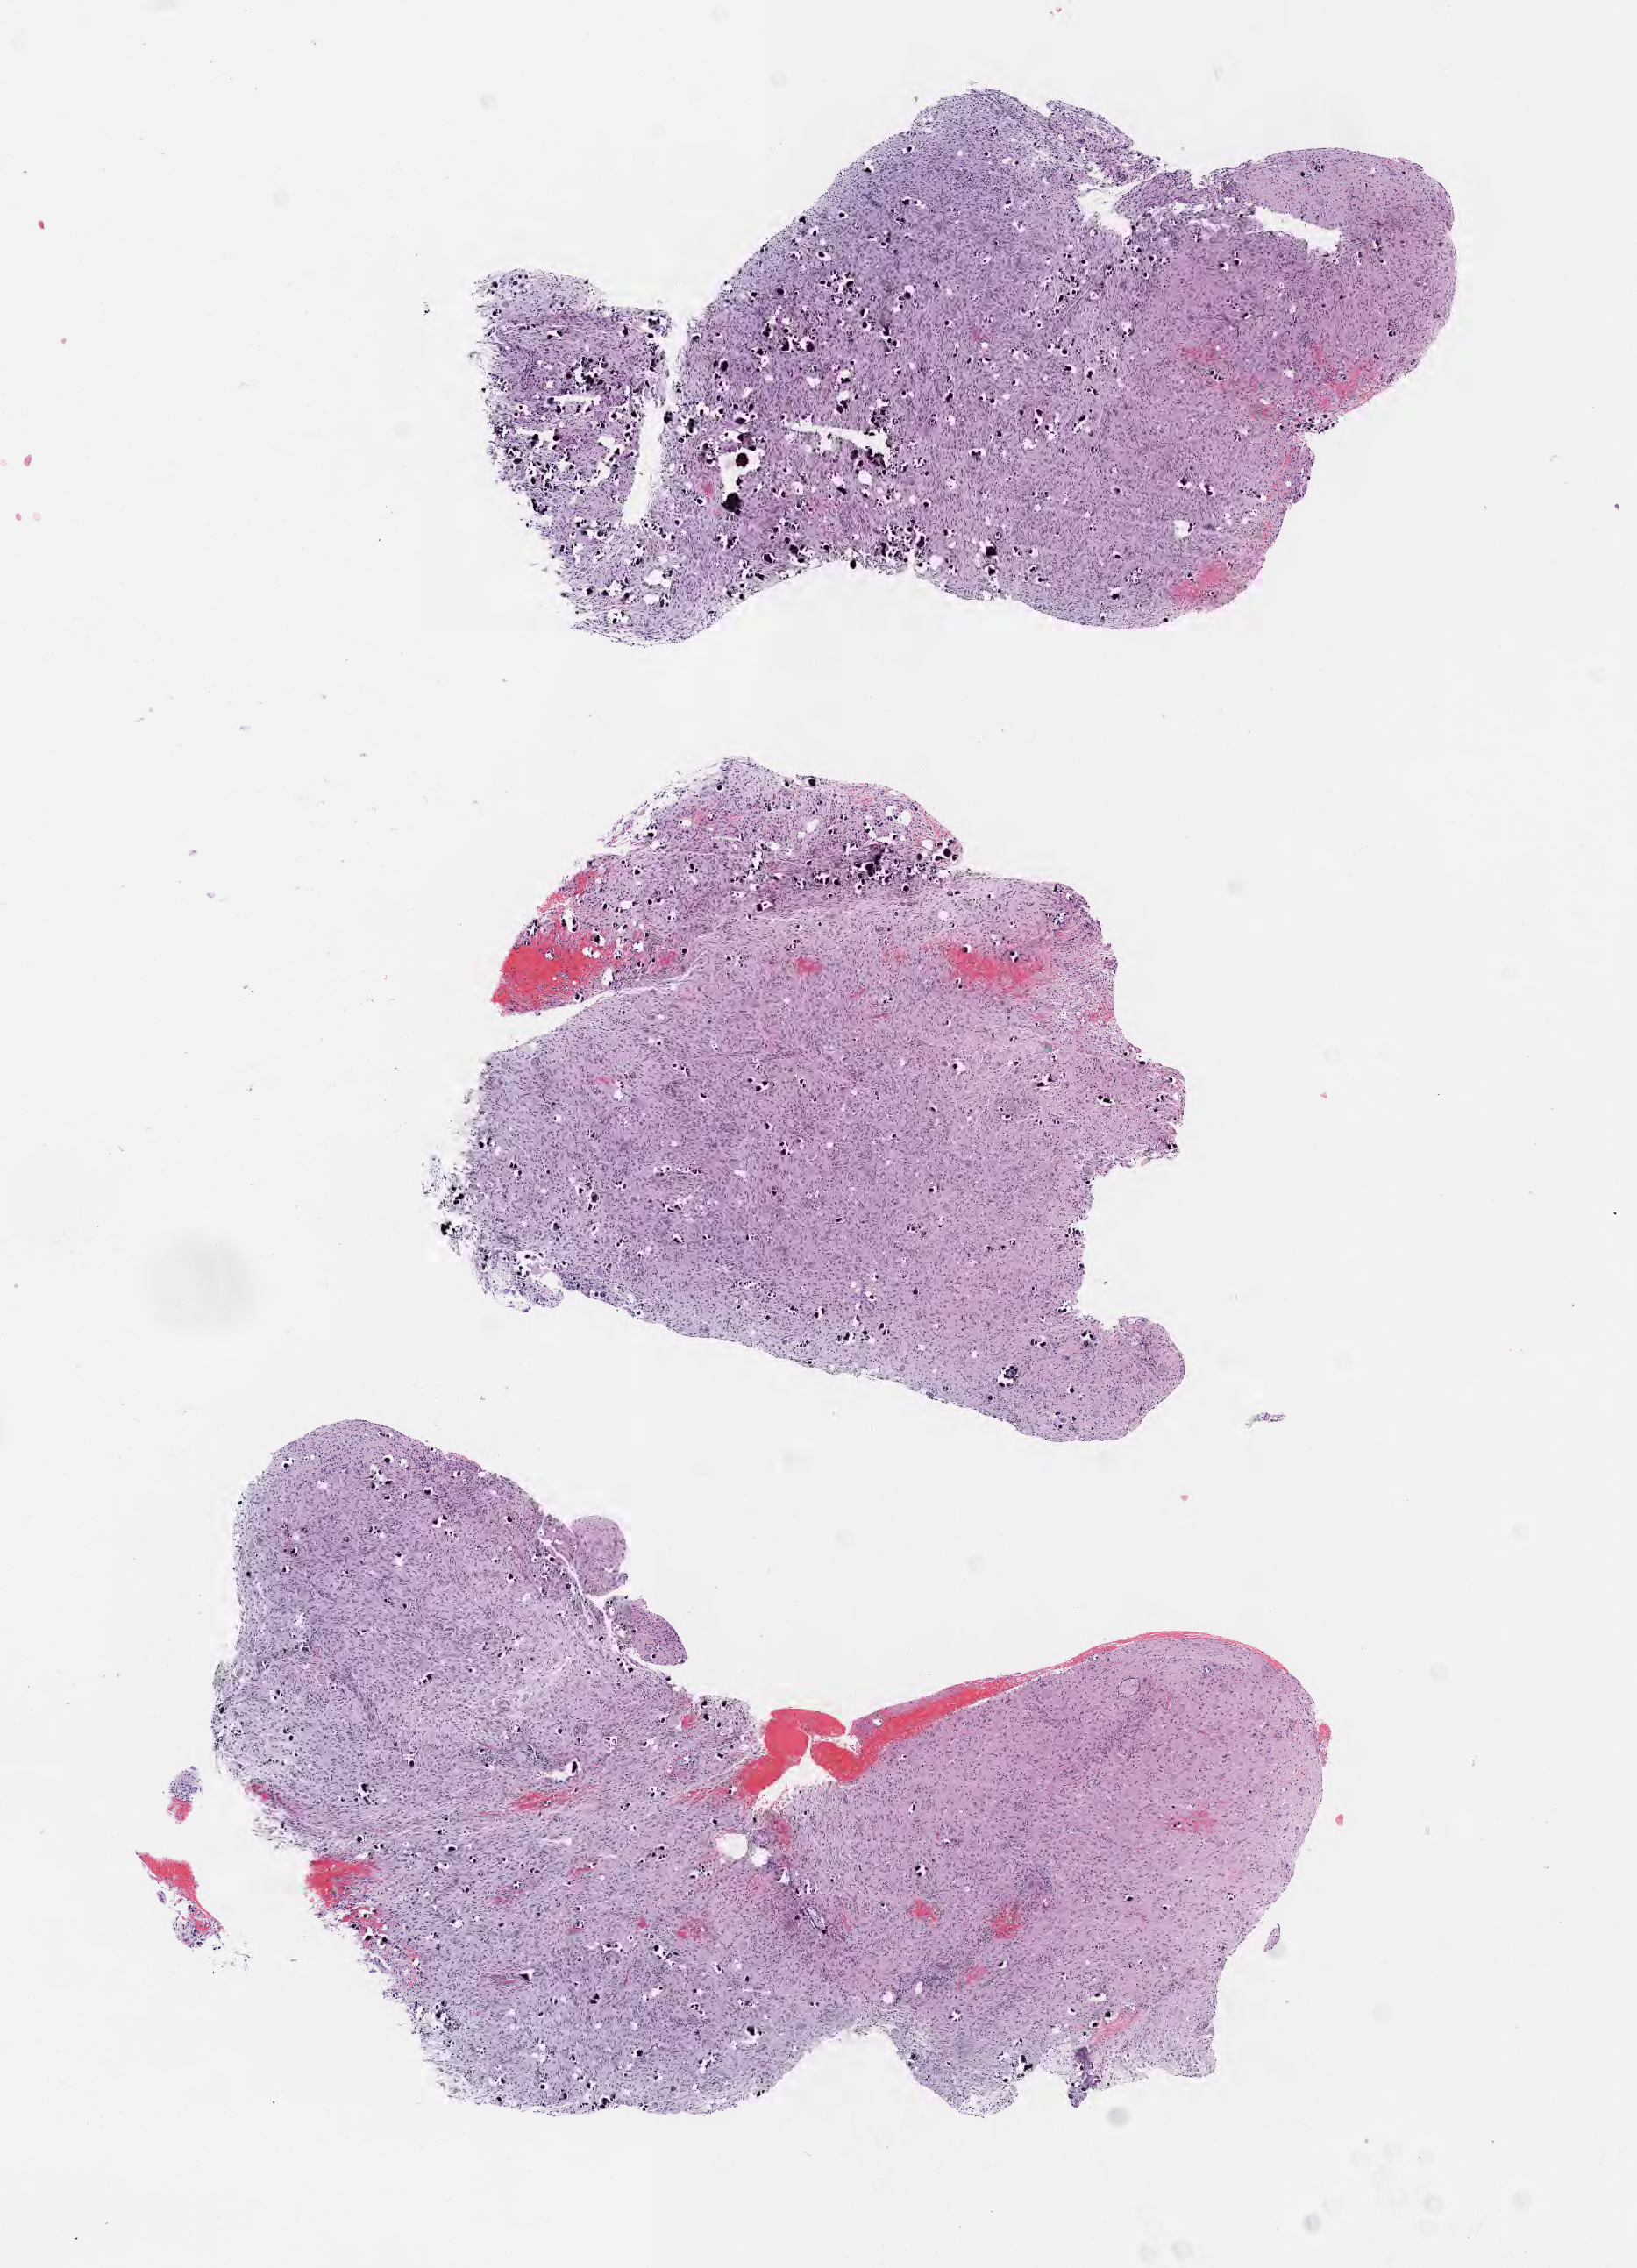
Haematoxylin and eosin whole-slide image of tumor tissue from the brain, low-resolution overview of the scanned area, about 7.6 x 10.5 mm; FFPE section. Patient: female, age 47 months (3 years 11 months).
Diagnosis: Neoplasm, malignant.